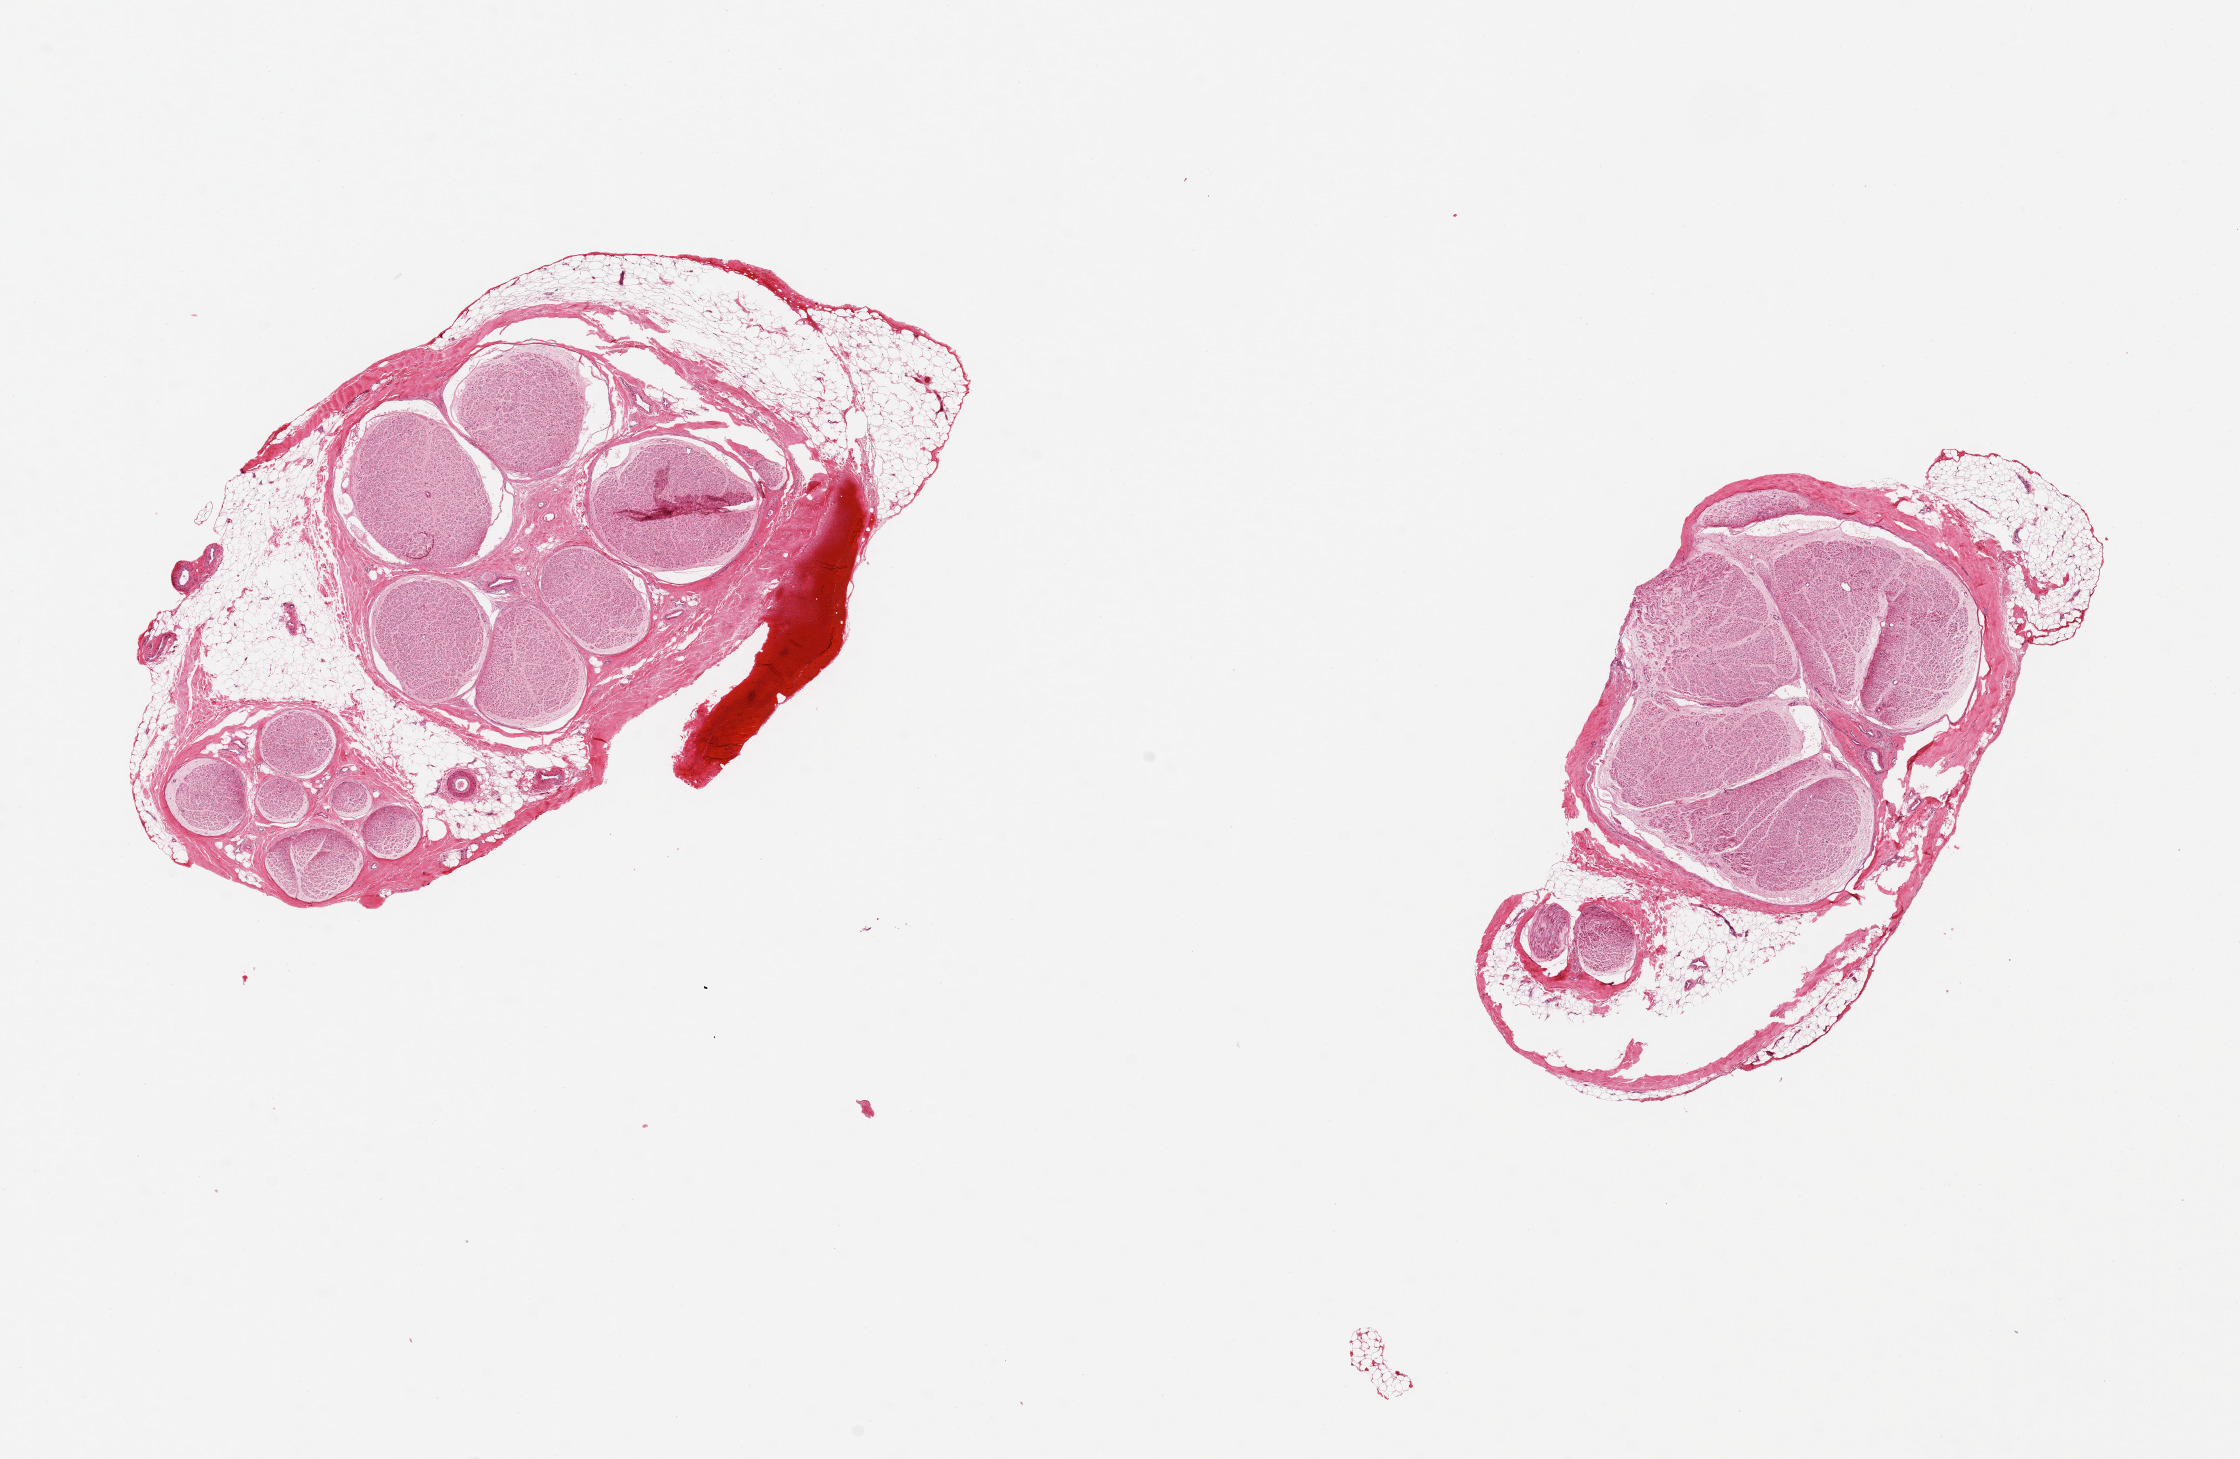
Digitized H&E-stained section, brightfield — low-resolution overview of the scanned area, about 17.7 x 11.5 mm (acquisition: 20x scan); PAXgene-fixed, paraffin-embedded tissue; target tissue: tibial nerve; tissue donor sample. Male donor.
- pathologist's review note for this sample: 2 pieces ~4.5mm d; Discontinuous rims of adherent fat around both ~0.5--1.5mm thick